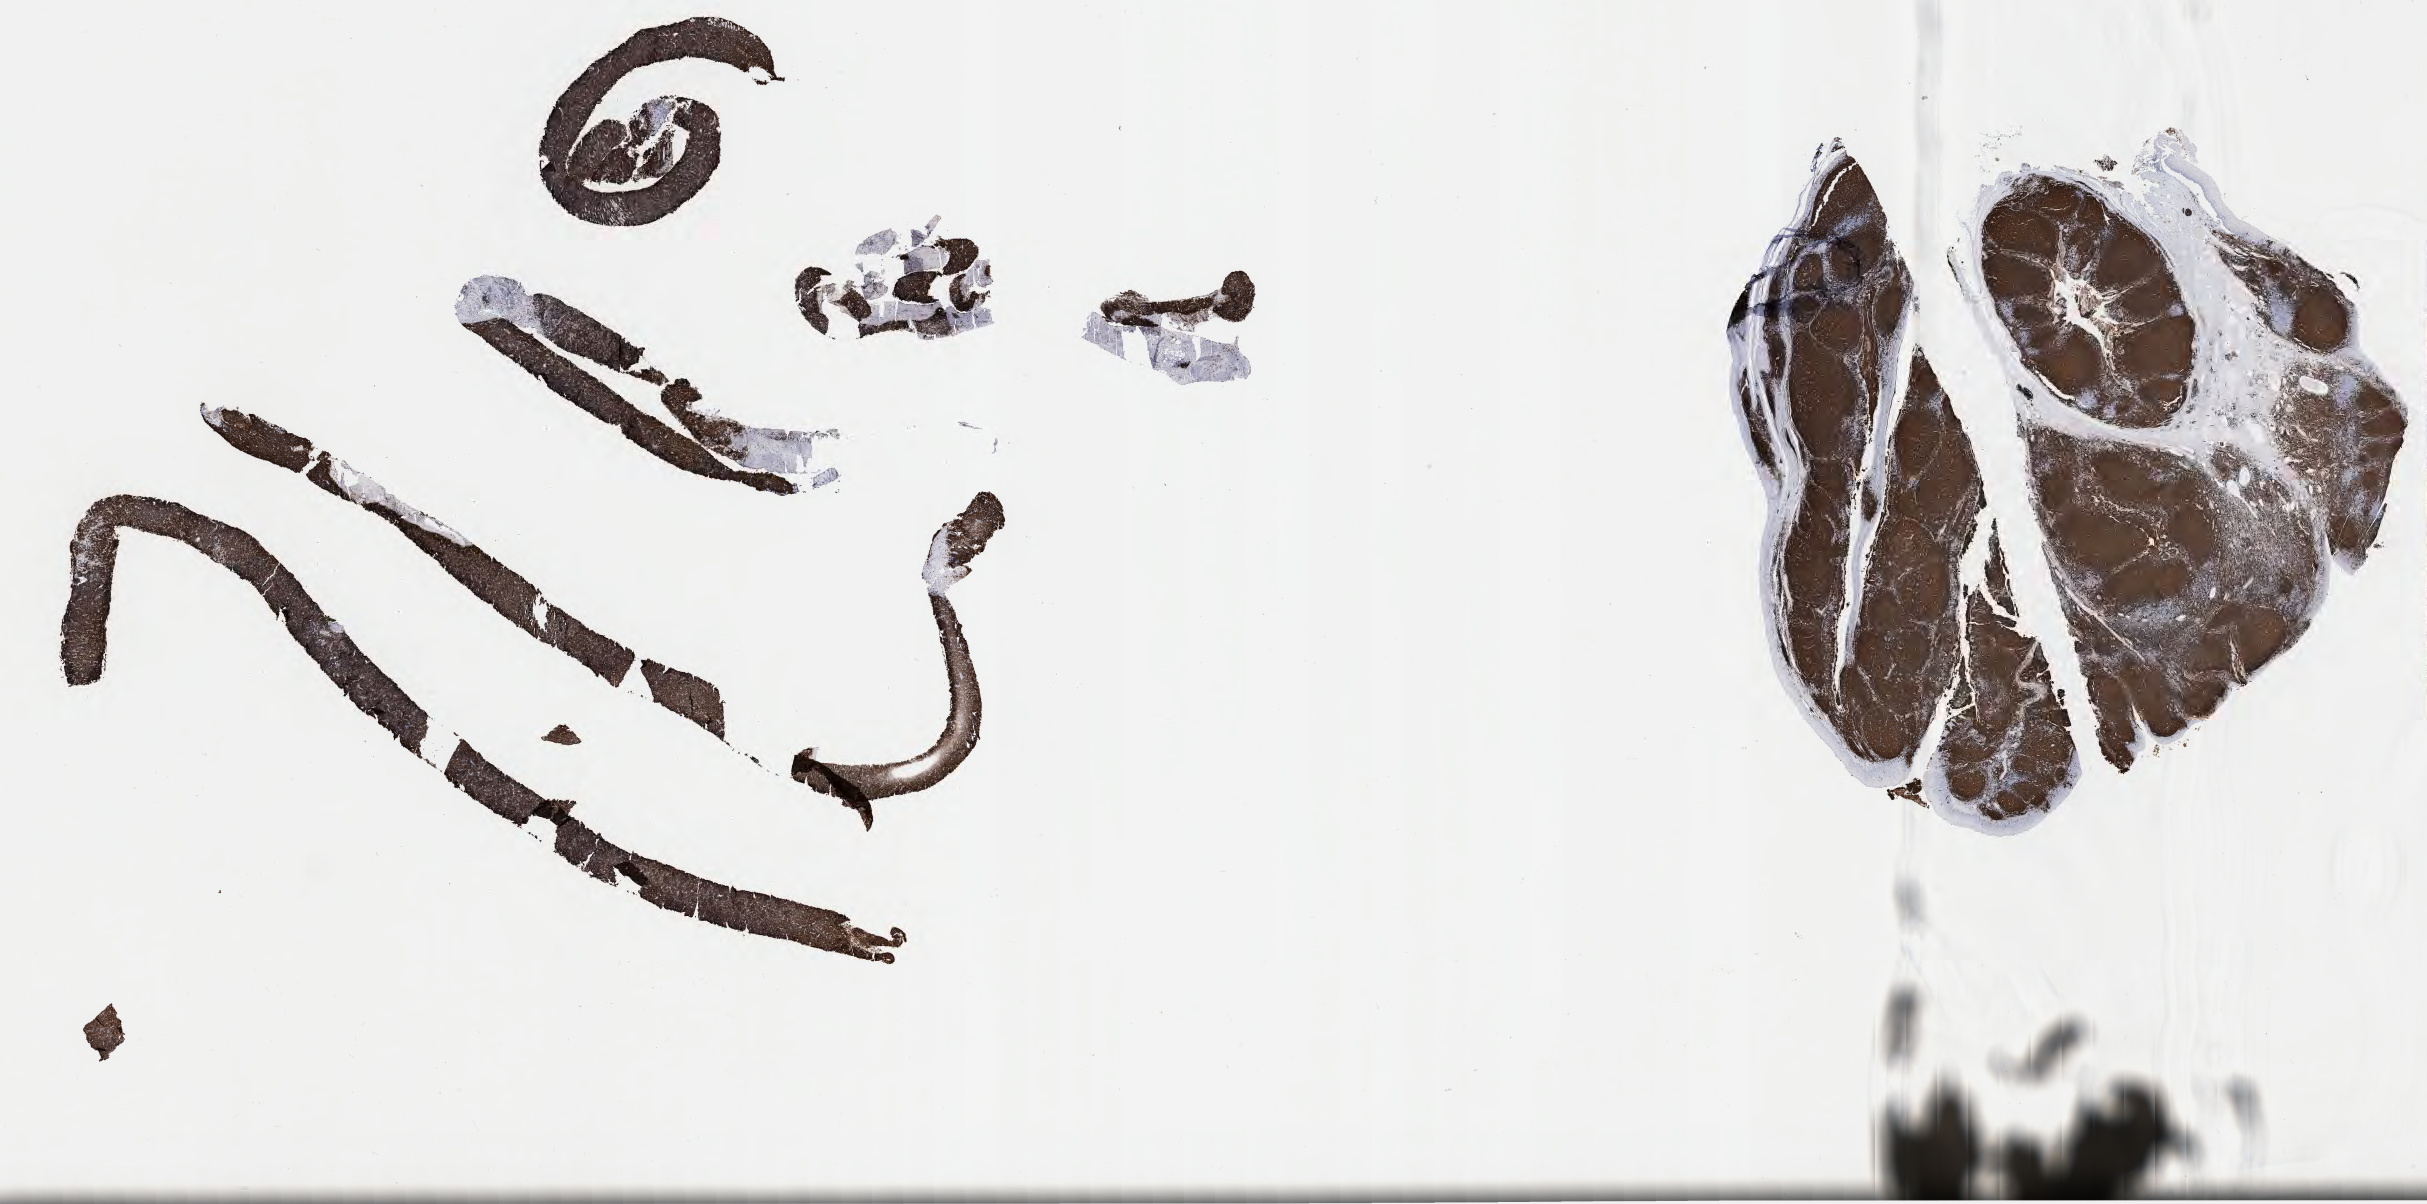
IHC for CD20, whole-slide image — shown as a low-resolution overview of the whole scanned area (about 39.3 x 19.5 mm), specimen: tumor tissue. Patient male; aged 45.
Histologic diagnosis: Burkitt lymphoma, NOS.